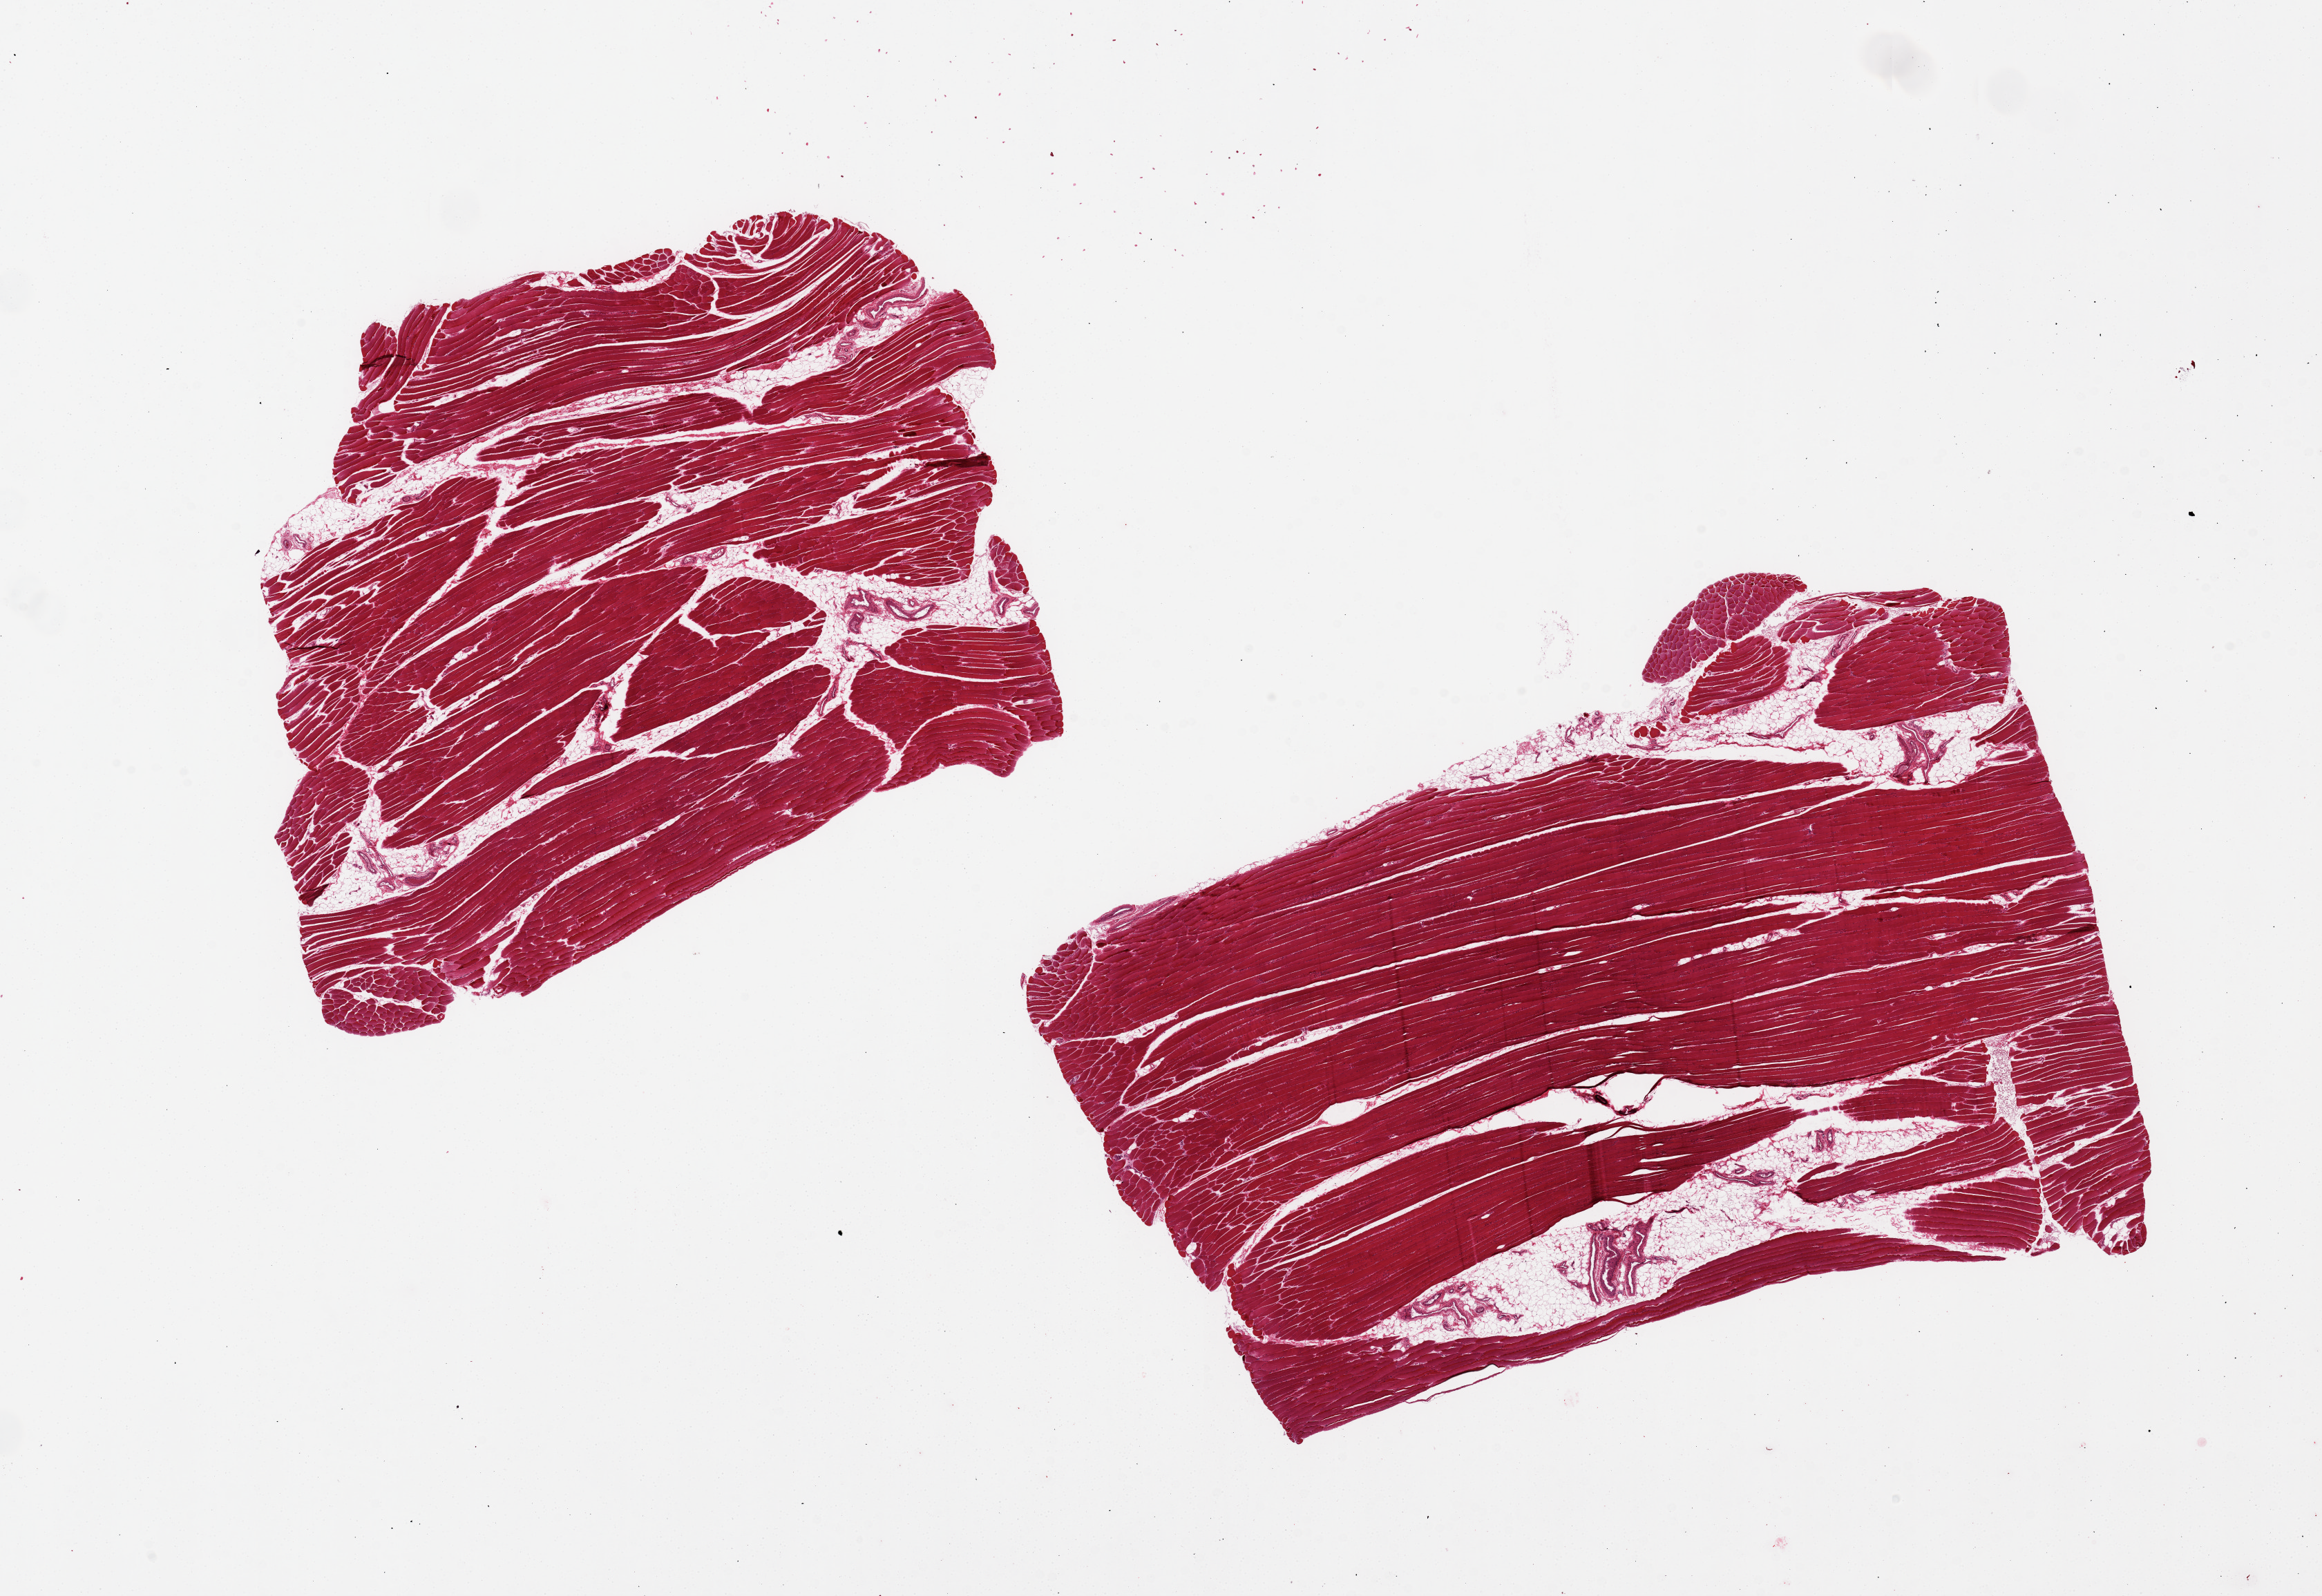
Whole-slide image, haematoxylin and eosin stain — a low-resolution overview of the entire scanned area, about 26.6 x 18.3 mm (acquisition: 20x scan), PAXgene-fixed paraffin-embedded (PFPE) section, sampled site (target tissue): skeletal muscle, donor tissue sample. Donor sex: male.
Reviewer comment on this tissue sample: 2 pieces, one with ~10% internal adipose tissue, the second with 10-20% internal adipose tissue.